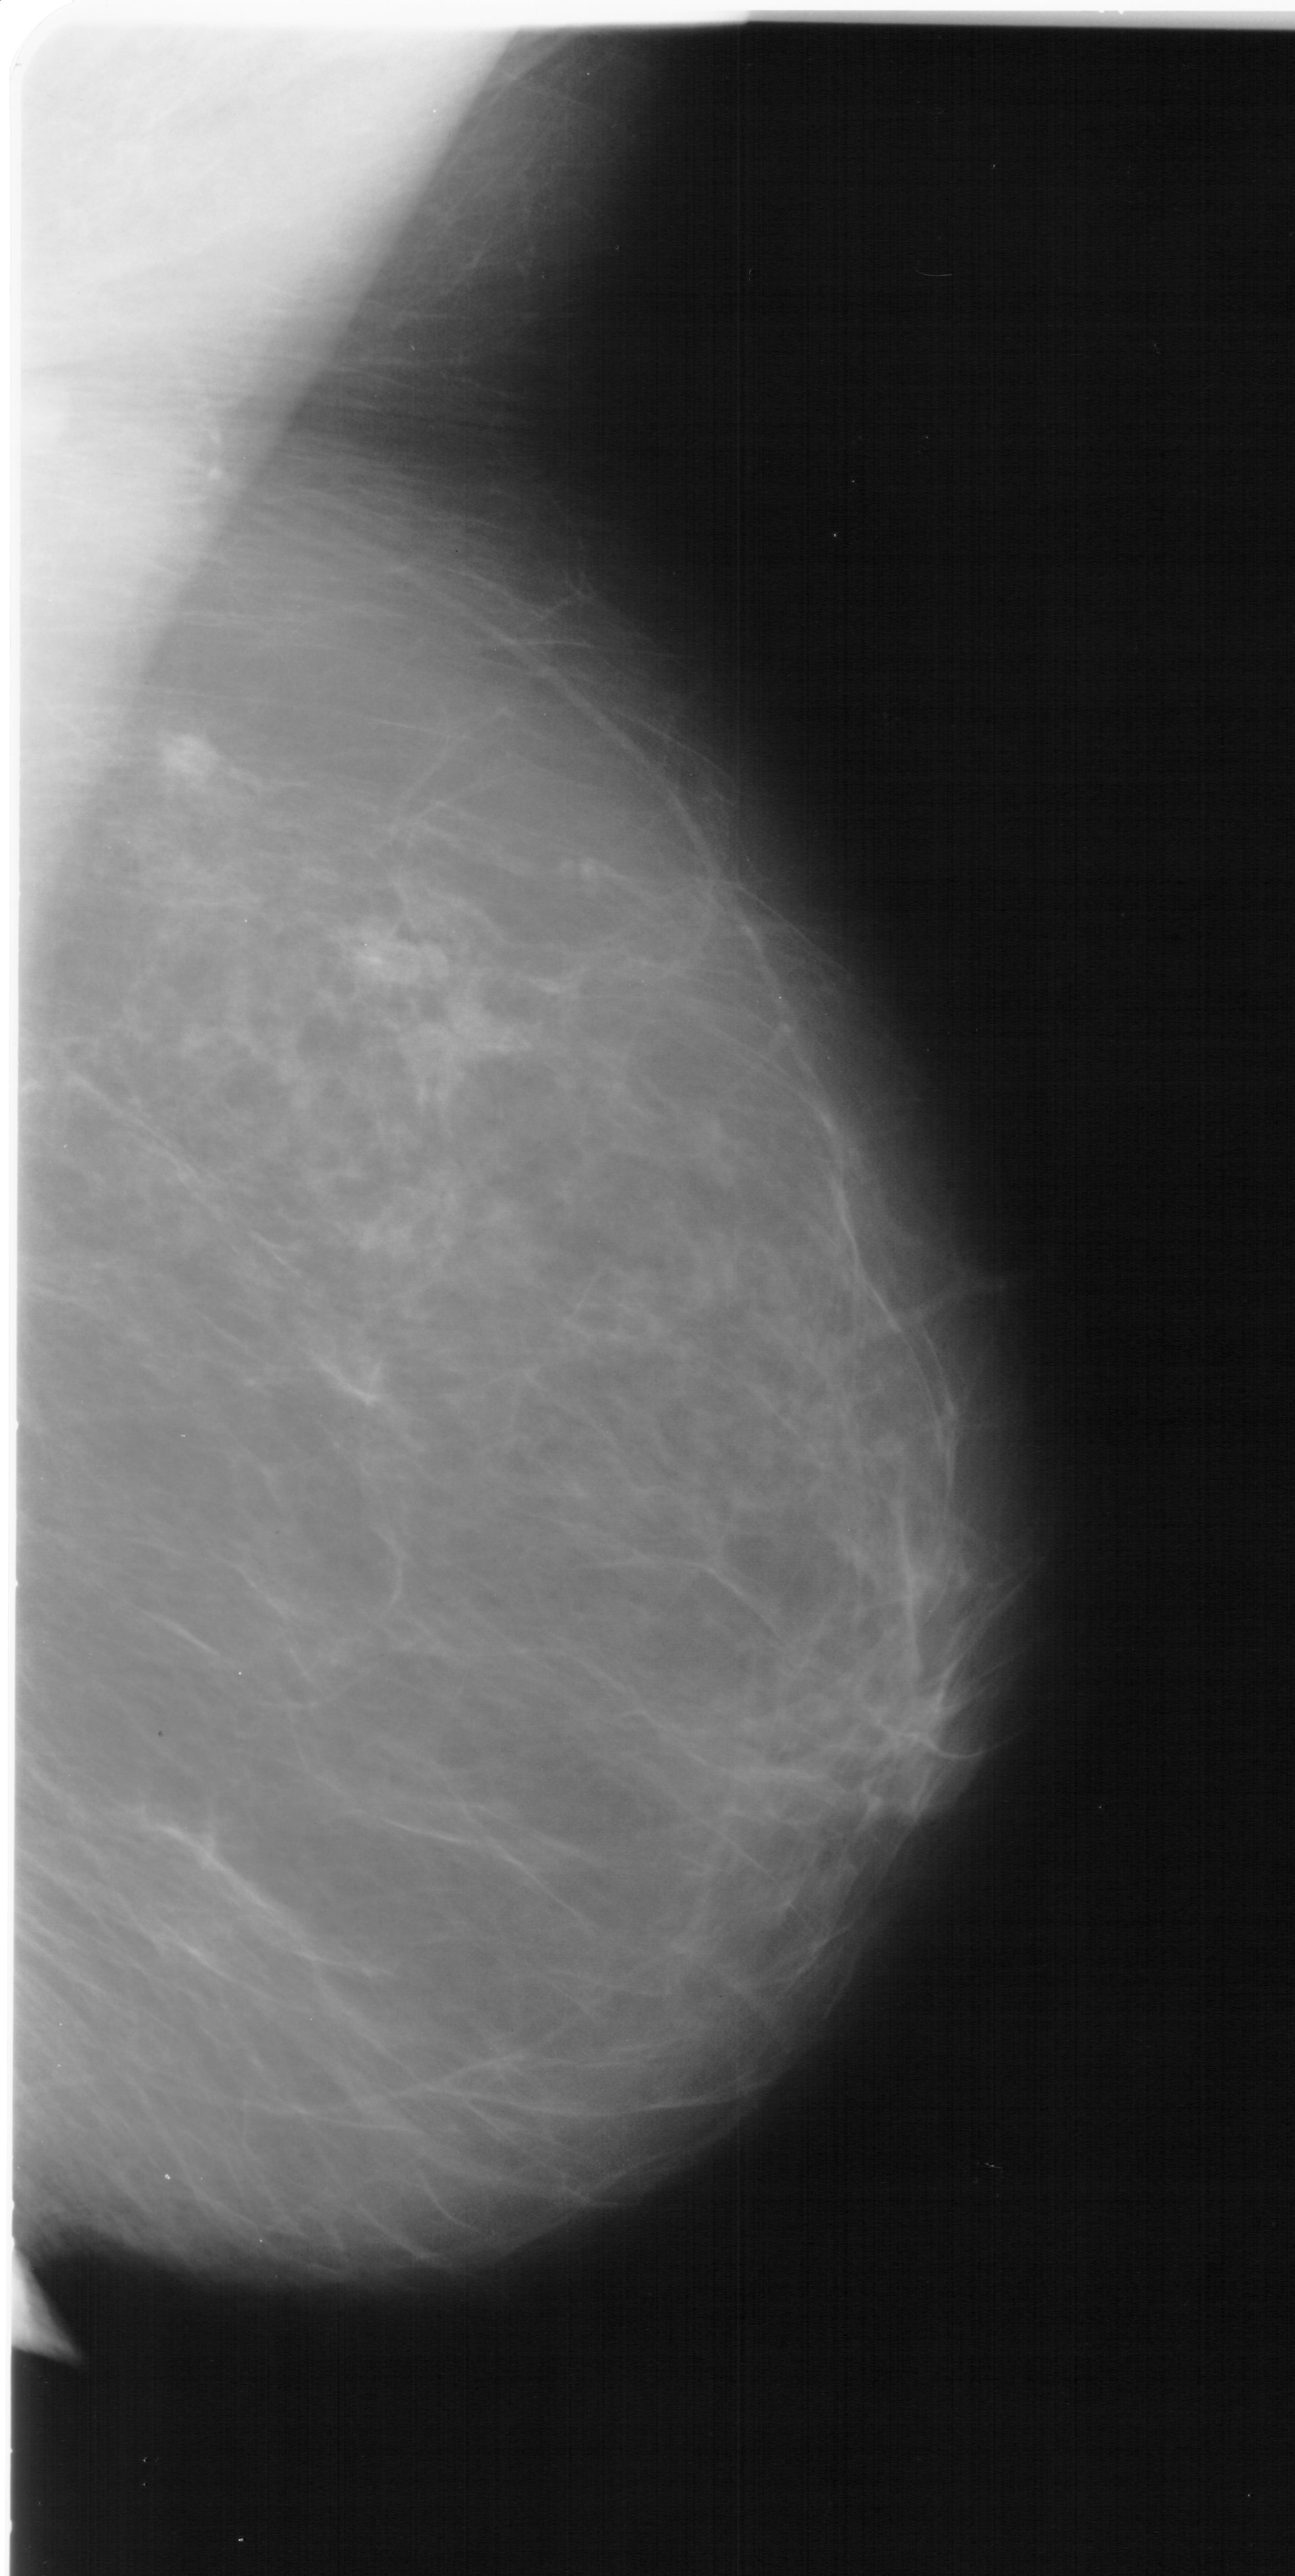
Digitized screen-film mammogram; right breast; mediolateral oblique (MLO) view; BI-RADS breast density category 2 (scale 1–4); 1295 × 2576 image matrix.
Expert-marked regions of interest on this film, with their recorded descriptors:
- mass, shape irregular, margins ill defined; BI-RADS assessment category 4; pathology (as recorded): malignant: bounding box (x1, y1, x2, y2) in pixels: (350, 920, 573, 1151)